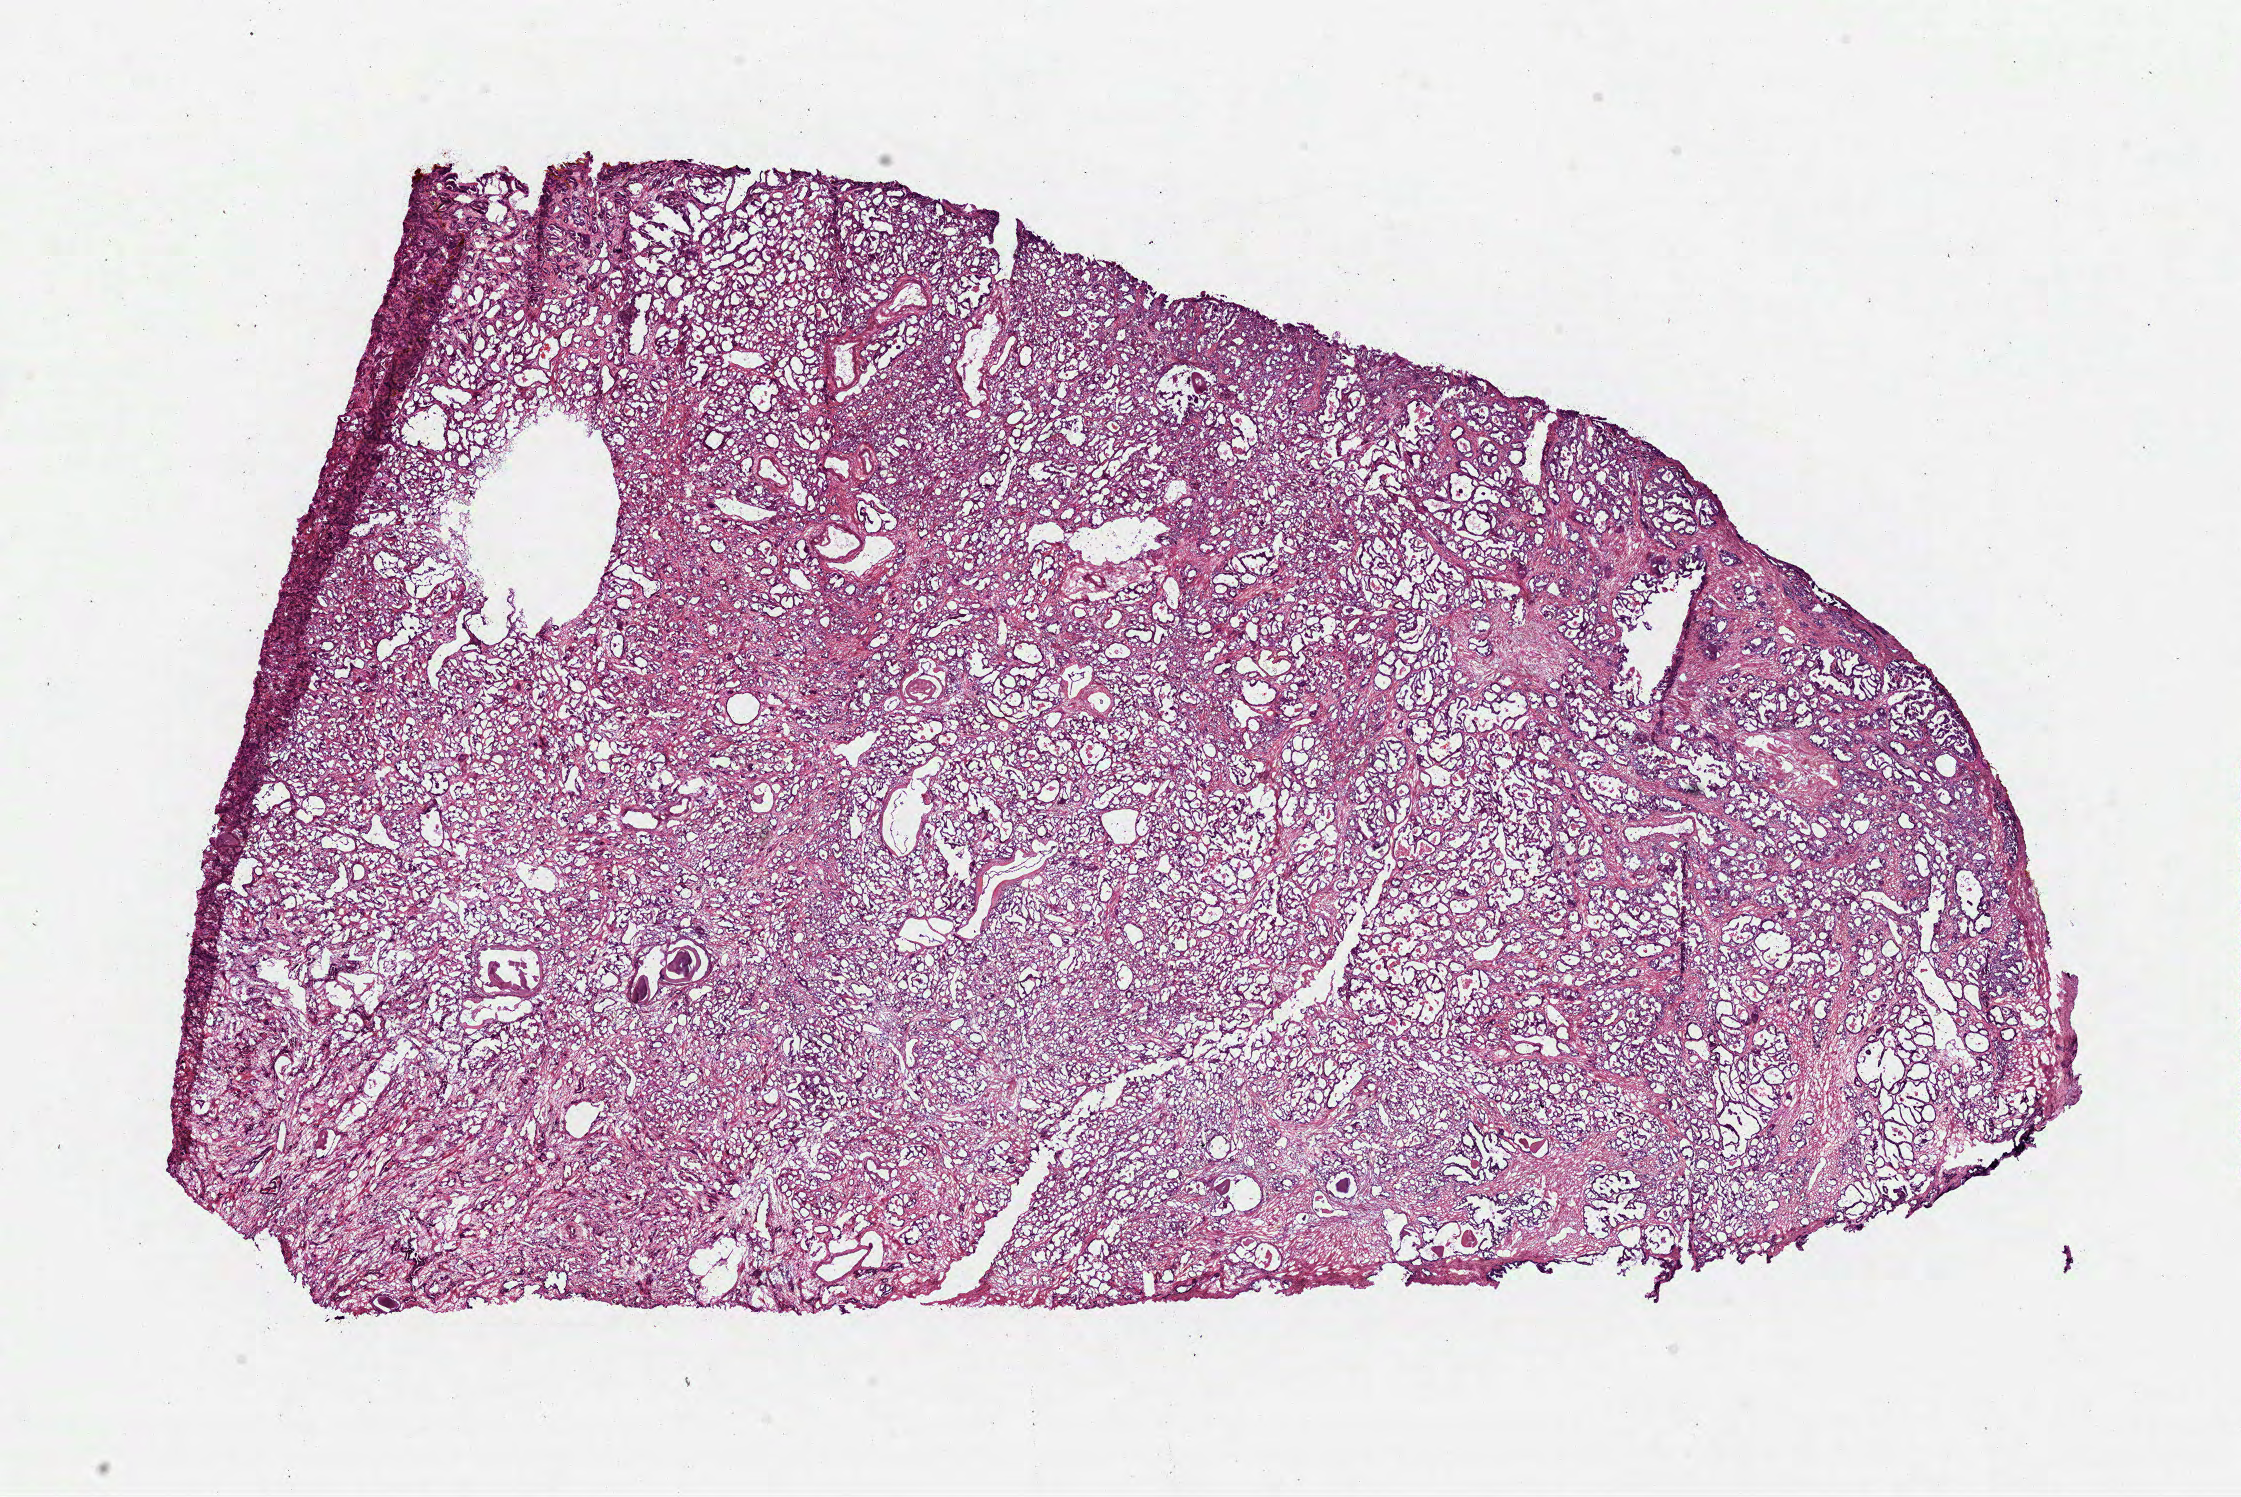
H&E whole-slide image — a low-resolution overview of the entire scanned area, about 18.1 x 12.1 mm (from a 40x scan). Frozen section from the bottom of the tissue portion. Prostate, primary tumour sample. Patient: male, age at initial diagnosis 61 years. Gleason score: 7 (4+3). Slide review estimates, as recorded: tumour cells 75%, tumour nuclei 80%, normal cells 12%, stromal cells 13%, necrosis 0%. Infiltration values recorded for this section: lymphocyte infiltration 2%, monocyte infiltration 0%, neutrophil infiltration 0%.
Diagnosis: Acinar cell carcinoma.